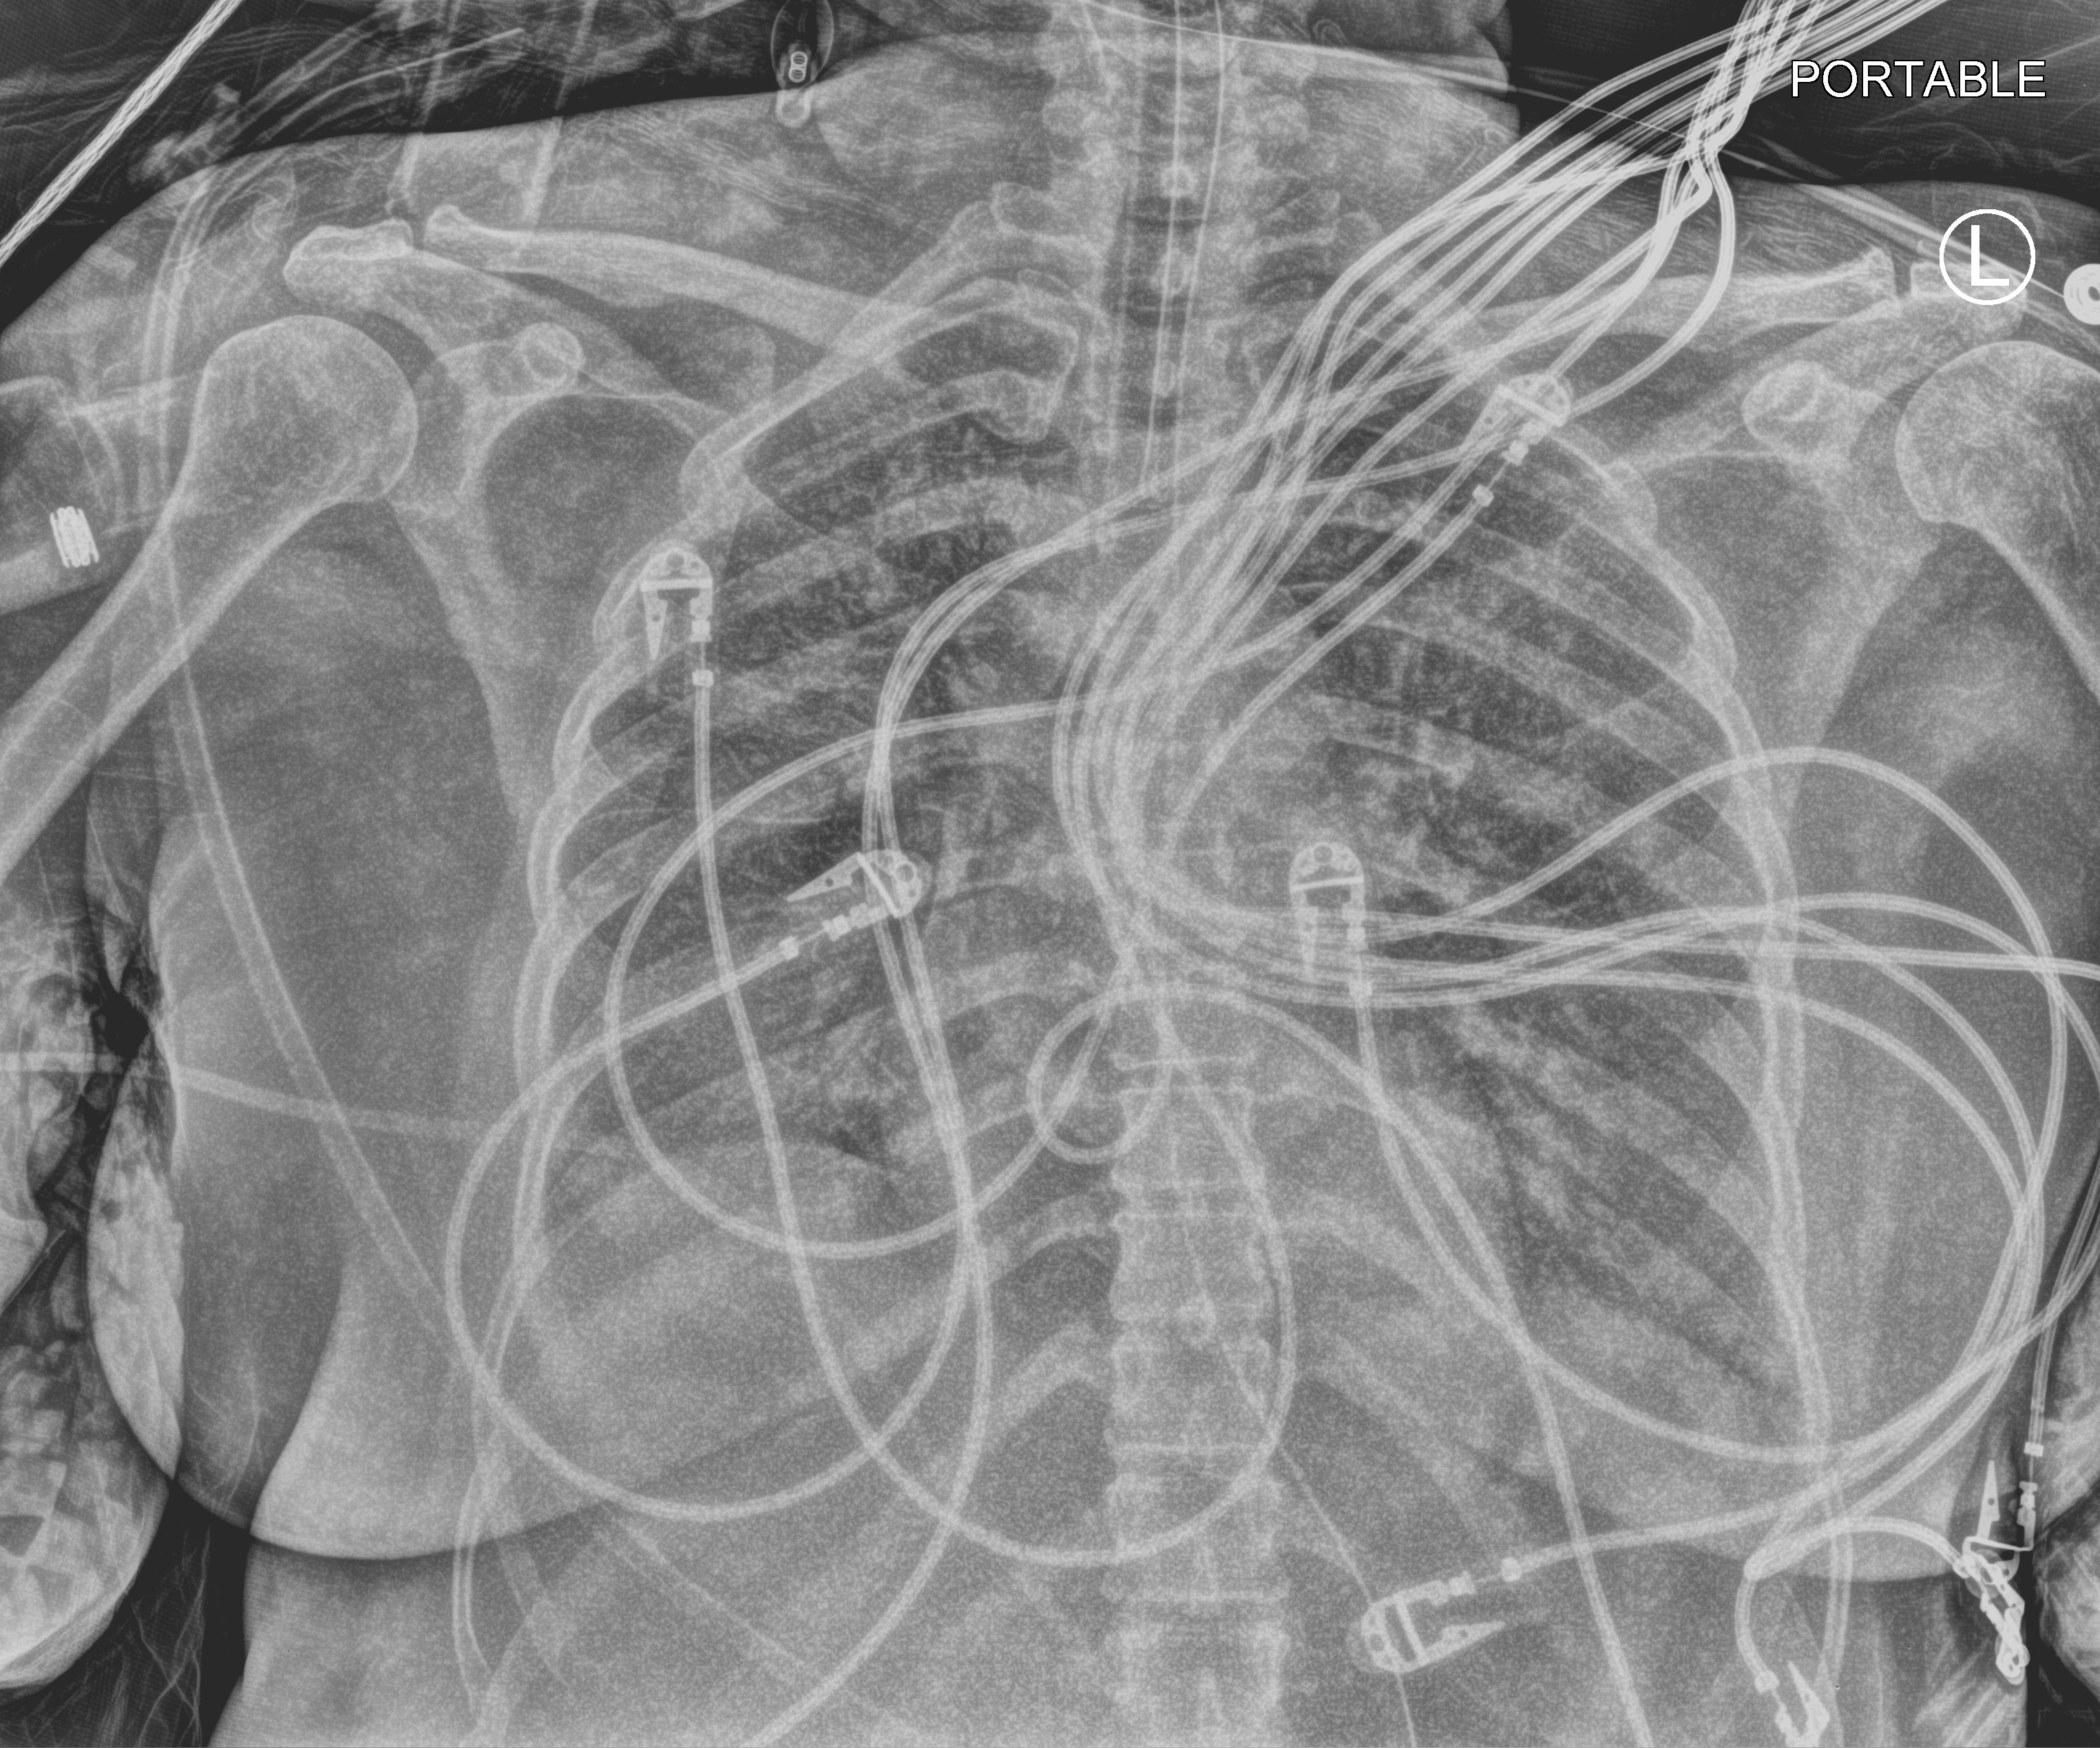
Bedside chest radiograph (computed radiography); anteroposterior (AP) projection. Male patient hospitalised with COVID-19, age 18–59 years.
From the hospital-stay record, not from the radiograph (when in the stay this image was taken is not recorded):
- hypertension (admission record): yes
- mechanically ventilated during this hospital stay: yes
- length of hospital stay: 38 days